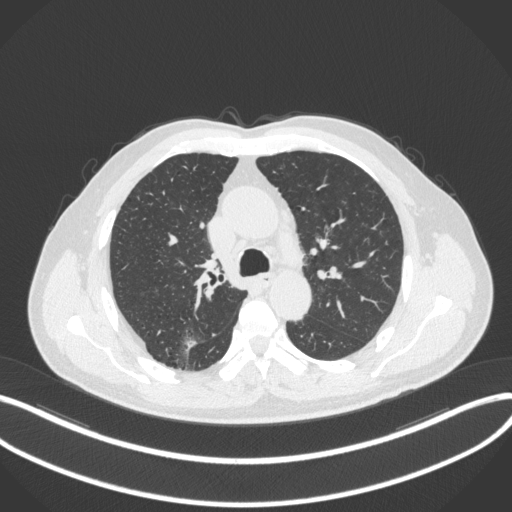
Chest CT, one axial slice; position 250 of 366 along the scan axis; 120 kVp; lung window (W 1500 / L -600 HU); 1 mm slice thickness; 512 × 512 image matrix, field of view 400 × 400 mm. Male patient, age 69 years. From the clinical record (not read from this slice): clinical TNM (as recorded): T1b N0 M0; histopathological grade: G2-3.
Structures marked on this image (bounding box drawn by a radiologist):
- lung tumour (recorded histology: adenocarcinoma): box from (x=181, y=336) to (x=201, y=350) px